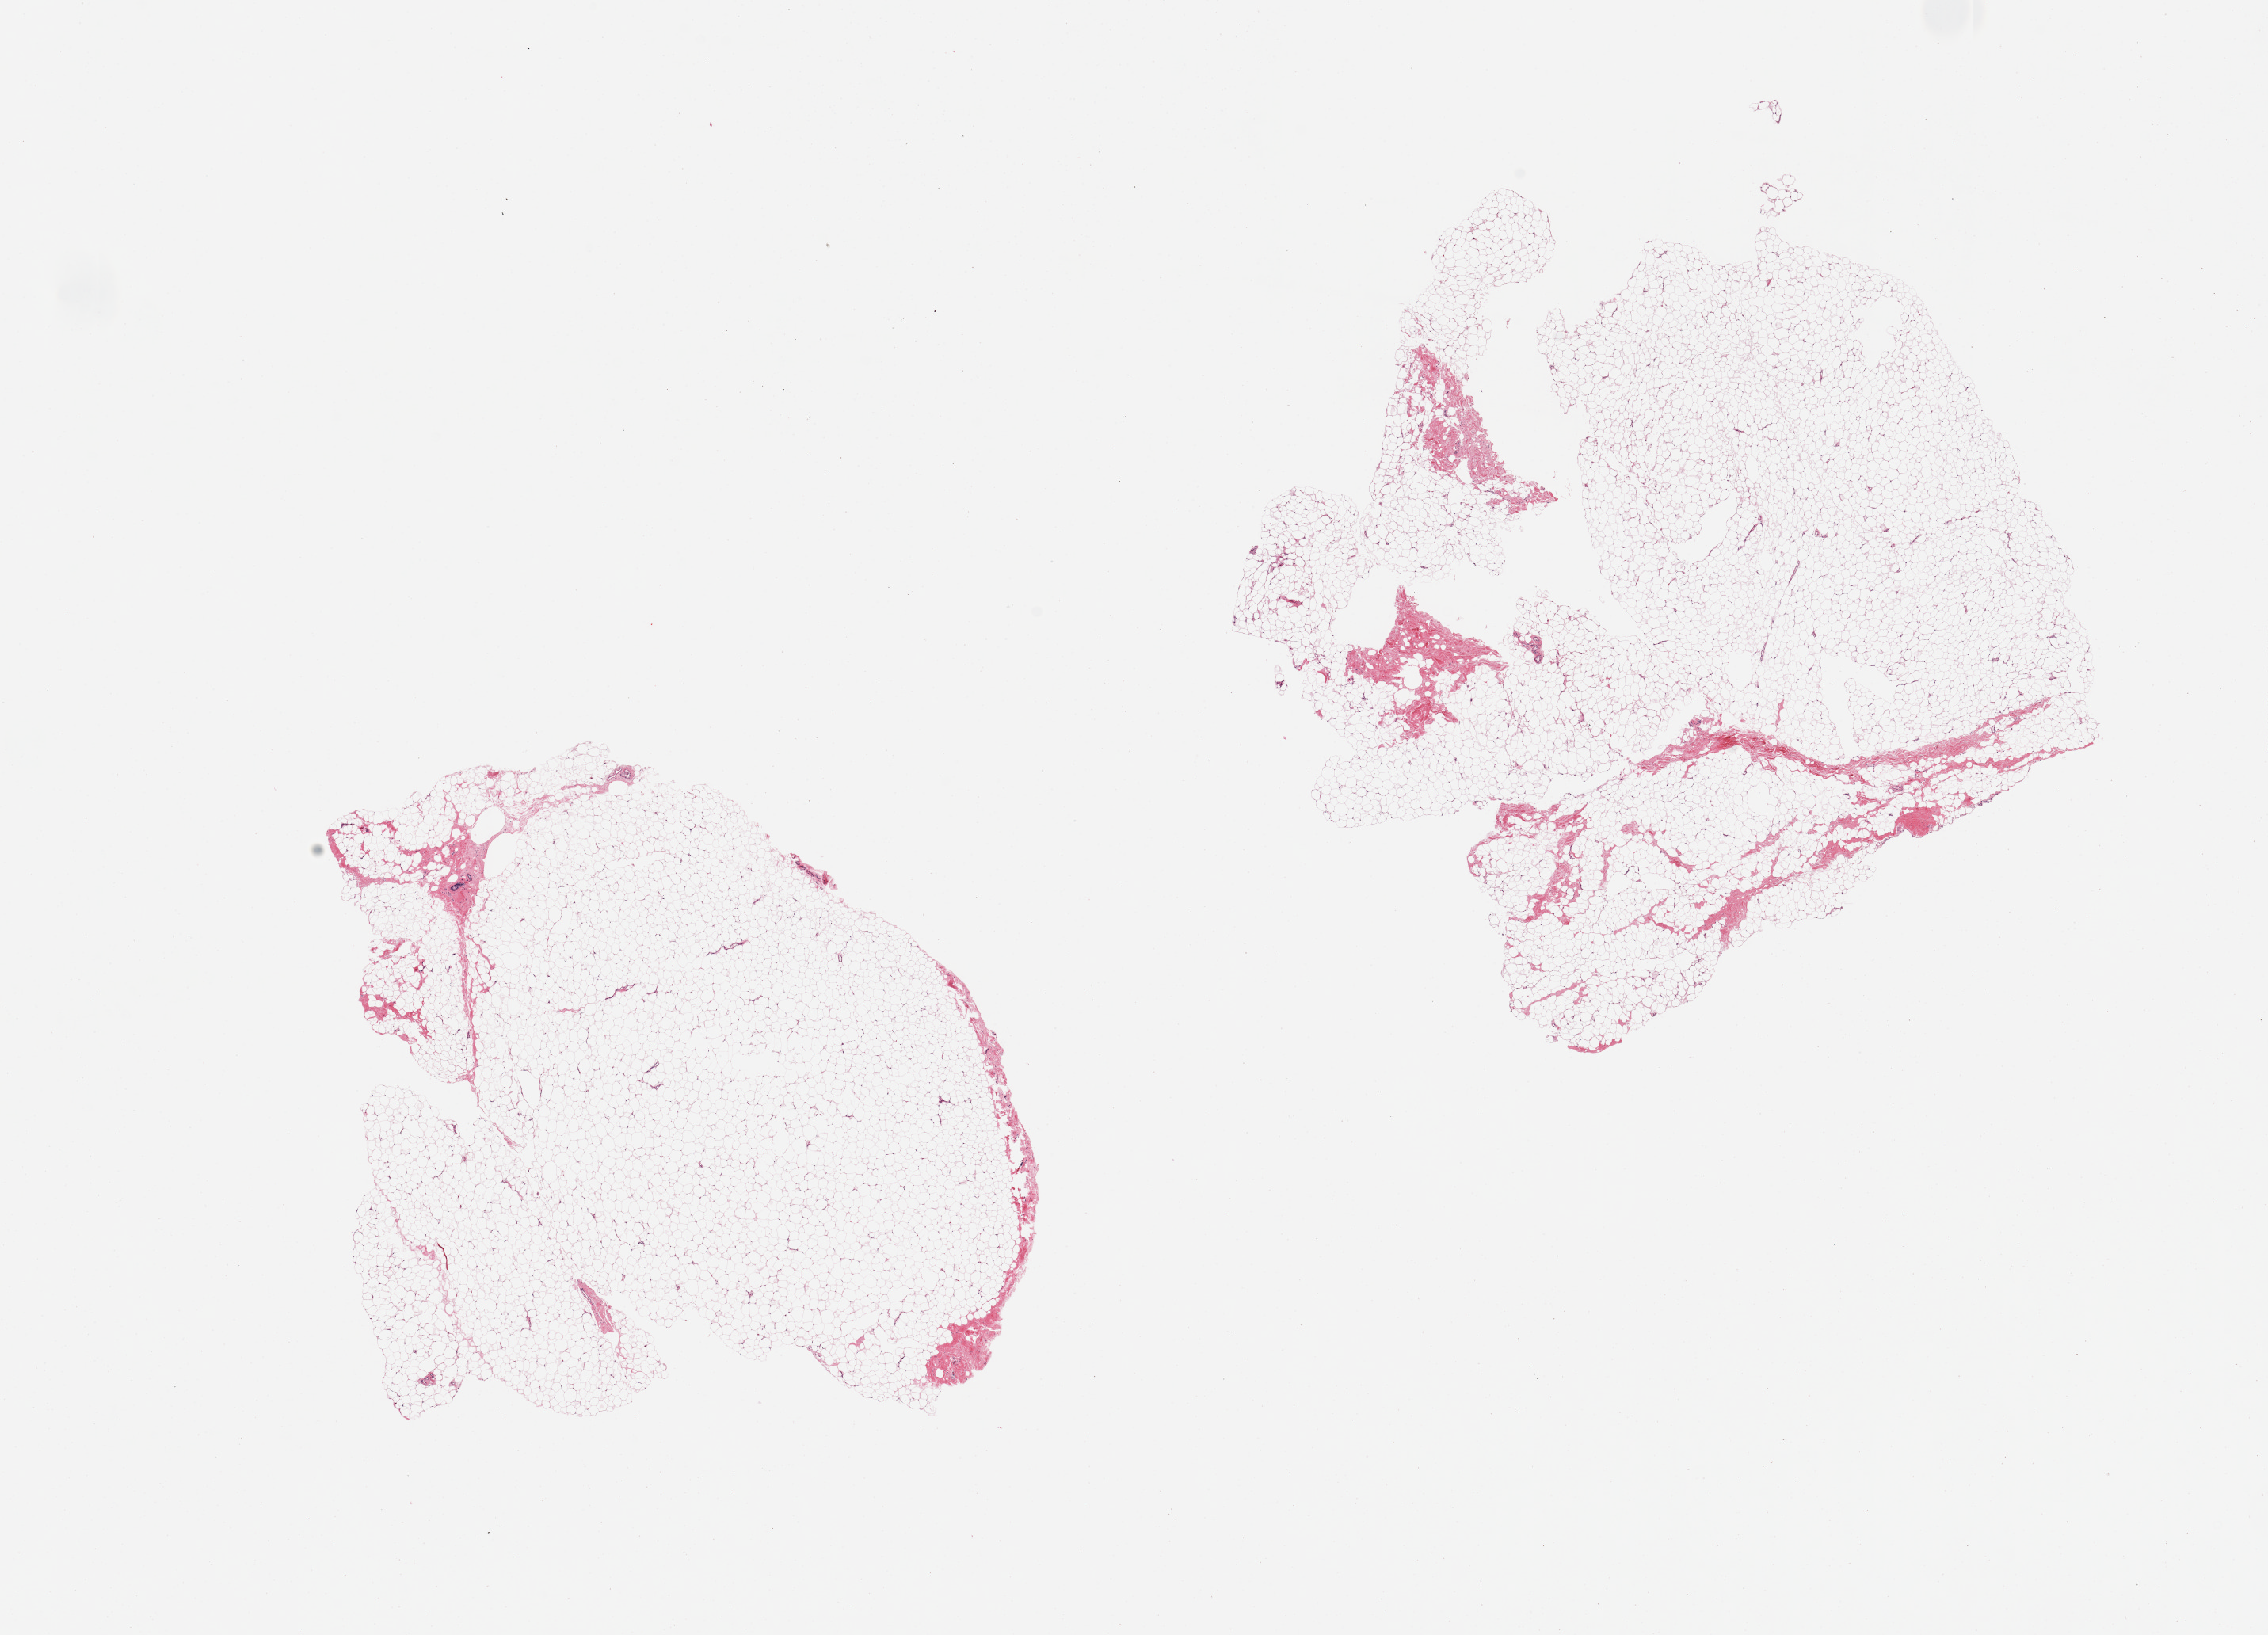
Hematoxylin and eosin (H&E) whole-slide image — low-resolution overview of the scanned area, about 22.6 x 16.3 mm; PAXgene-fixed, paraffin-embedded tissue; target tissue: breast; donor tissue sample. Donor sex: male.
• review note (as recorded): 2 pieces. No ducts; mostly adipose